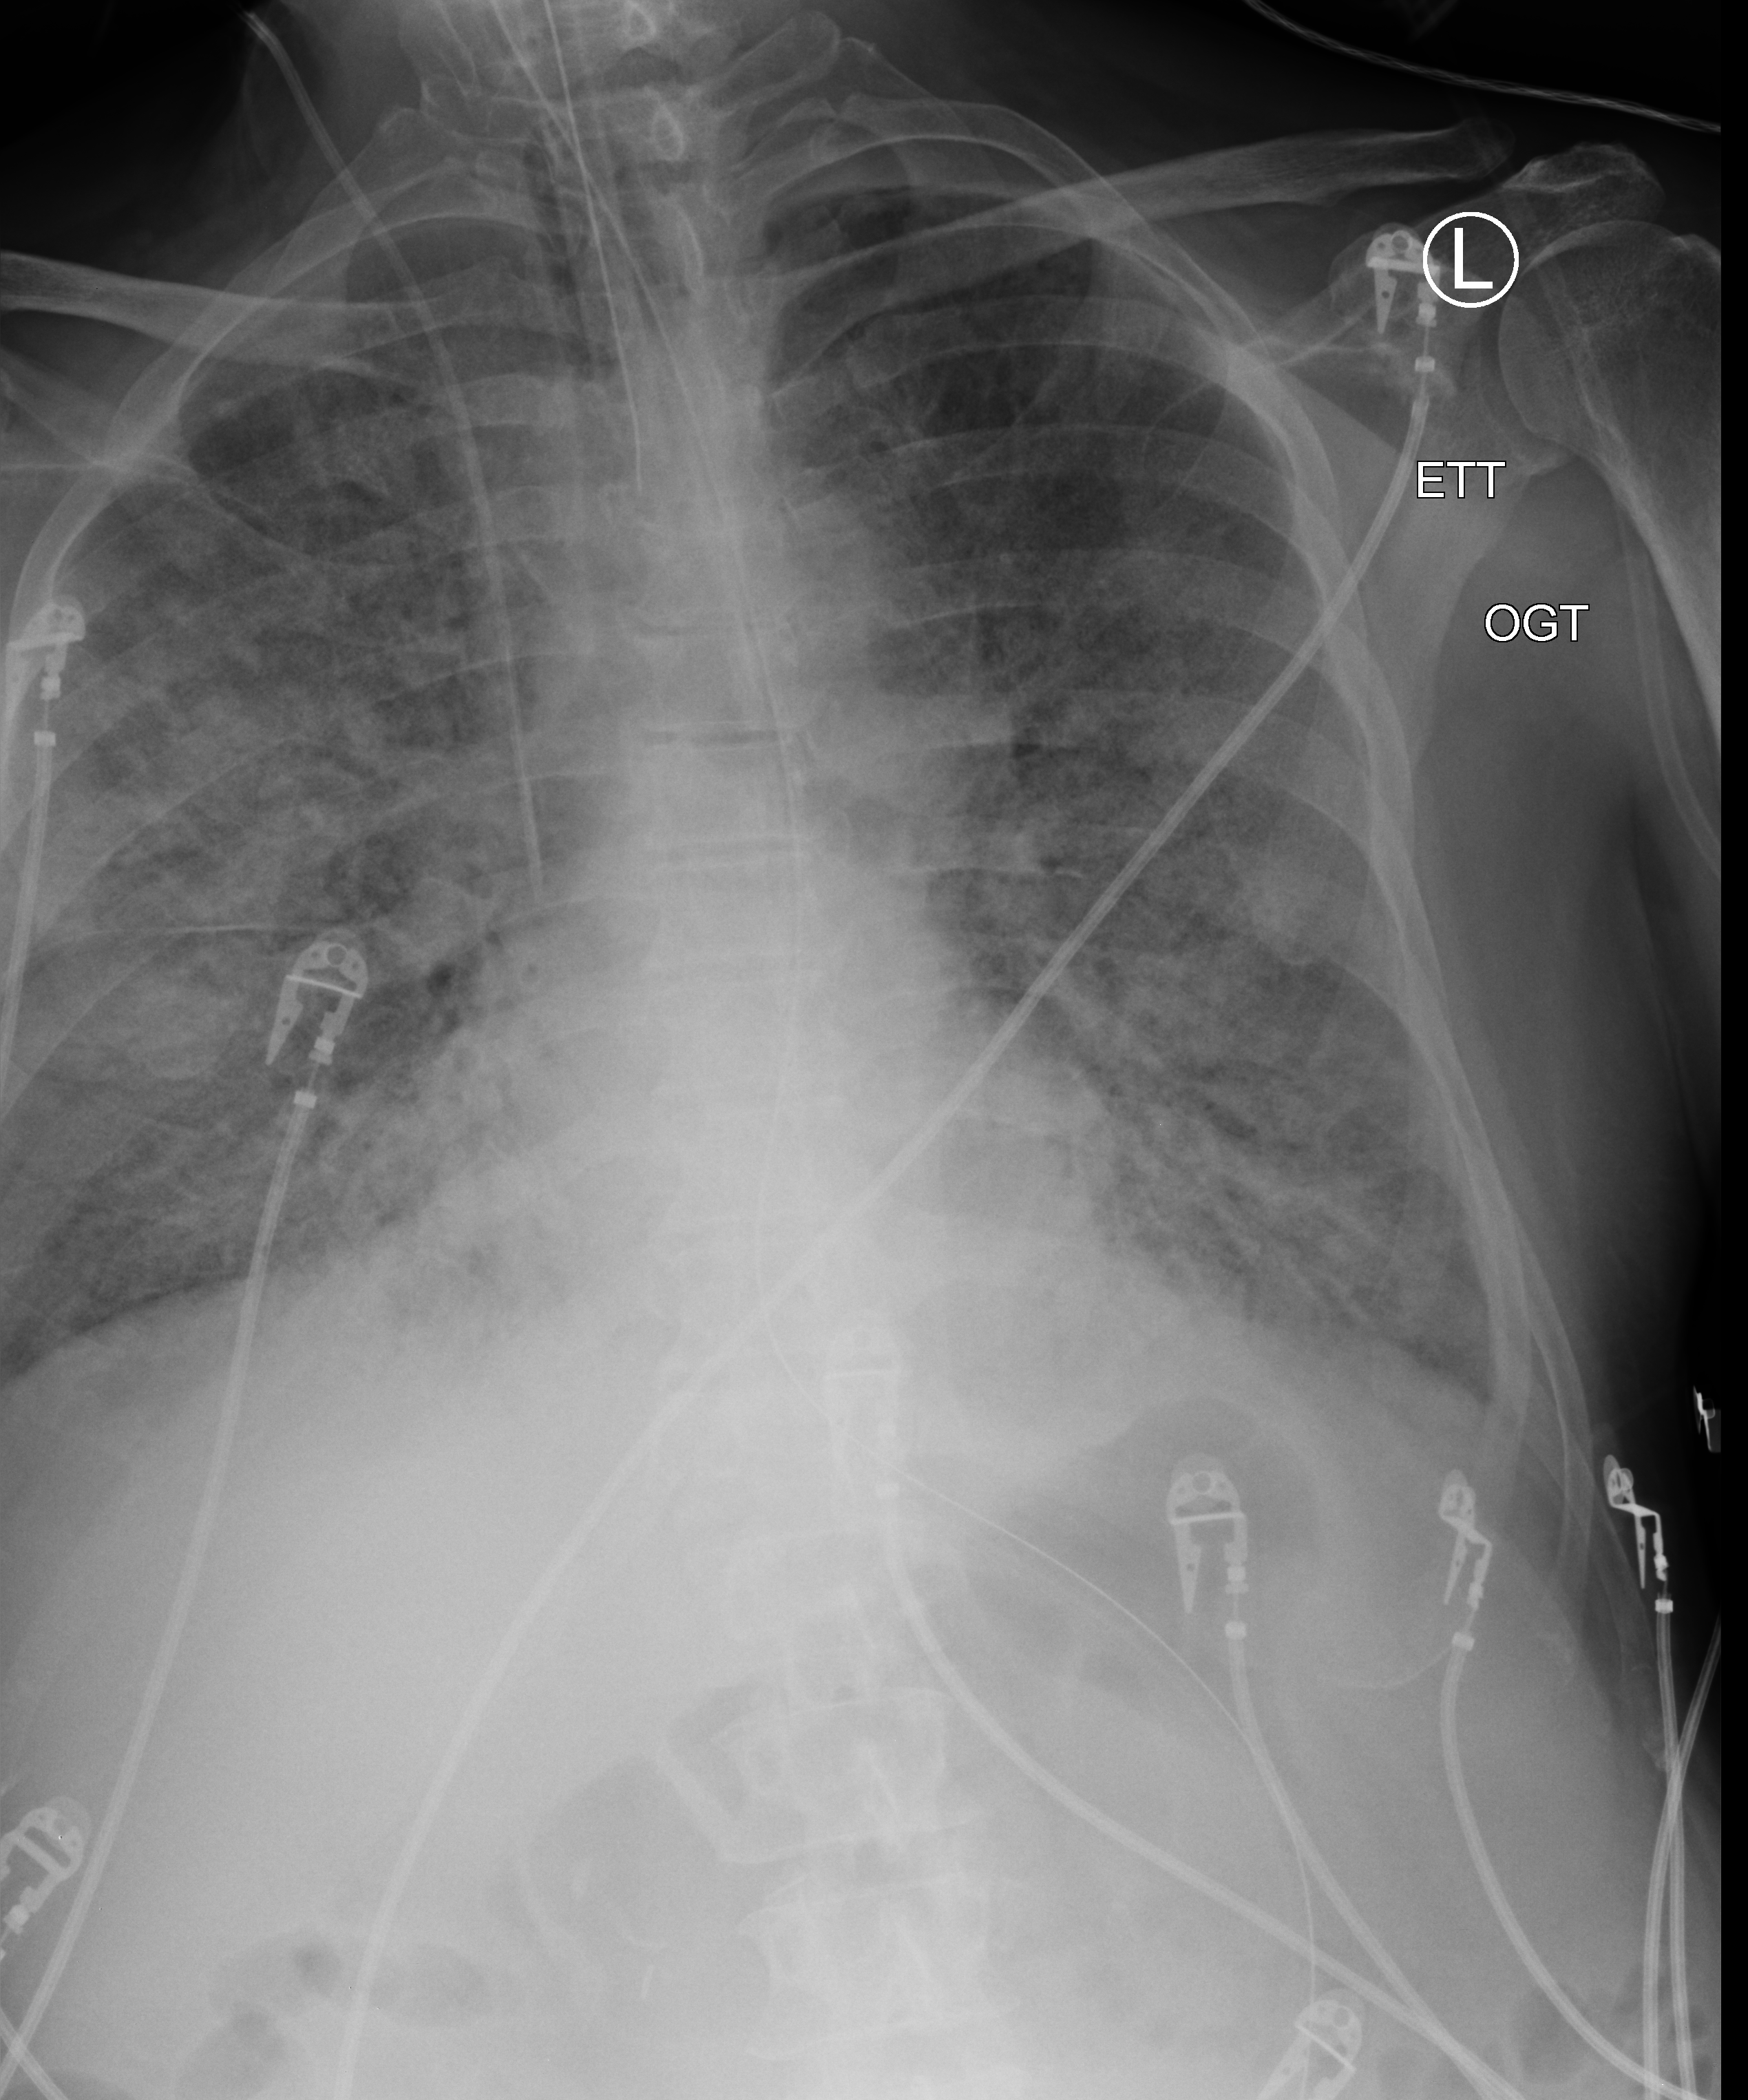
Chest X-ray (portable). Patient hospitalised with COVID-19; male, aged 60–74 years.
From the hospital-stay record, not from the radiograph (when in the stay this image was taken is not recorded):
- smoking status (admission record): former
- length of hospital stay: 24 days